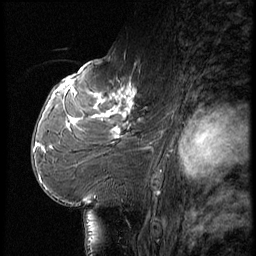
Breast MRI (dynamic contrast-enhanced), one sagittal slice. Dynamic contrast-enhanced series, image 2 of 3 at this slice position (ordered by acquisition). 1.5 T. TE 4.2 ms, TR 9 ms. 2.5 mm slice thickness. 256 × 256 image matrix. Female patient, age 61 years. Case-level facts recorded for this patient, not image findings: setting: breast cancer imaged before/during neoadjuvant chemotherapy; receptor status: HR-positive, HER2-negative.
Structures marked on this image (semi-automatically segmented with operator editing):
- analysis volume of interest (the breast-tissue region the enhancement analysis was run in; not a lesion): bounding box [x1, y1, x2, y2] px = [65, 74, 149, 175]
- tumour enhancement mask (voxels above the 140 % enhancement threshold inside the analysis volume of interest): [70, 85, 137, 139]